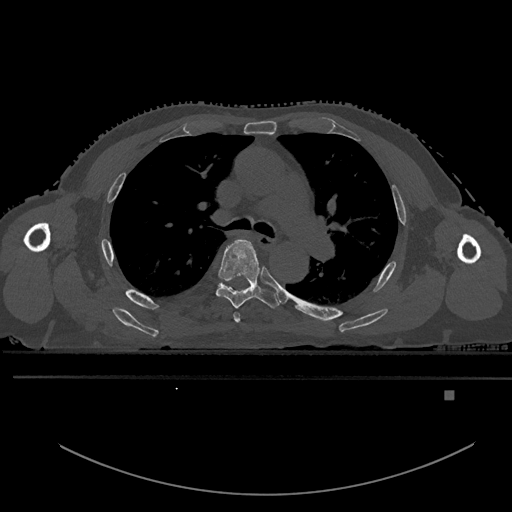
CT including the spine, one axial slice; position 361 of 969 along the scan axis; bone window (W 1800 / L 400 HU); 0.5 mm slice thickness; 512 × 512 image matrix, field of view 456 × 456 mm. Patient: male, 82 years. Case-level facts recorded for this patient, not image findings: primary cancer: prostate; vertebrae with lytic lesions (as recorded): T11, T9, T8, T2.
Outlined on this slice (semi-automatic segmentation, software-assisted and operator-edited):
- T4 vertebra: bounding box [x1, y1, x2, y2] px = [233, 312, 240, 323]
- T5 vertebra: [216, 239, 280, 309]